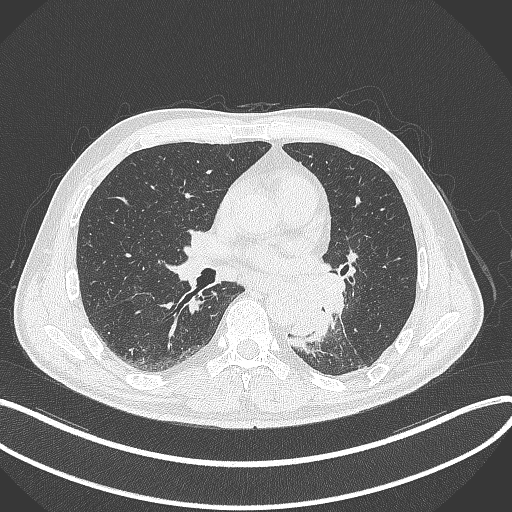
Chest CT, one axial slice; 120 kVp; lung window (W 1500 / L -600 HU); 512 × 512 image matrix, field of view 400 × 400 mm. Male patient, age 59 years. From the clinical record (not read from this slice): clinical TNM (as recorded): T2a N2 M0.
Annotated regions visible in this slice (bounding box drawn by a radiologist):
- lung tumour (recorded histology: squamous cell carcinoma): box from (x=299, y=273) to (x=349, y=342) px